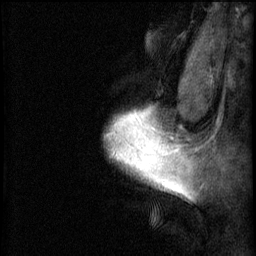
Breast MRI (dynamic contrast-enhanced), one sagittal slice; slice 55 of 60 in the series (ordered by position); 3 images stored at this slice position (order not interpretable as contrast timing); 1.5 T; TE 4.2 ms, TR 8.2 ms; 2 mm slice thickness; 256 × 256 image matrix, field of view 180 × 180 mm. Patient: female, 40 years.
Structures marked on this image (semi-automatically segmented with operator editing):
- analysis volume of interest (the breast-tissue region the enhancement analysis was run in; not a lesion): bounding box <111,106,167,191> (left, top, right, bottom; pixels)
- tumour enhancement mask (voxels above the 70 % enhancement threshold inside the analysis volume of interest): <111,110,167,191>